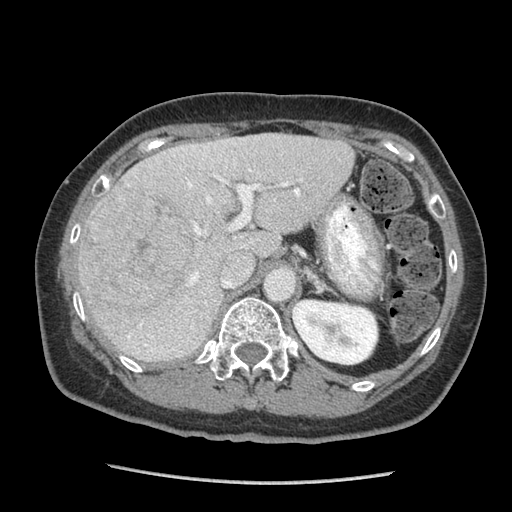
Contrast-enhanced abdominal CT (liver protocol), one axial slice; slice 55 of 105 in the series (ordered by position); 140 kVp; soft-tissue window (W 400 / L 40 HU); 2.5 mm slice thickness; 512 × 512 image matrix. From the clinical record (not read from this slice): diagnosis: hepatocellular carcinoma (patient treated with transarterial chemoembolisation; whether this scan precedes or follows treatment is not stated here); TNM stage (as recorded): Stage-I; Child-Pugh class: A; tumour nodularity: uninodular; tumour size: 11.1 cm.
Outlined on this slice (semi-automatic segmentation, software-assisted and operator-edited):
- liver parenchyma outside the tumour (the mass and vessels are separate outlines, so this box may not span the whole liver): box from (x=78, y=134) to (x=354, y=362) px
- mass: (x=82, y=189)–(x=207, y=318)
- liver vessels: (x=127, y=146)–(x=303, y=351)